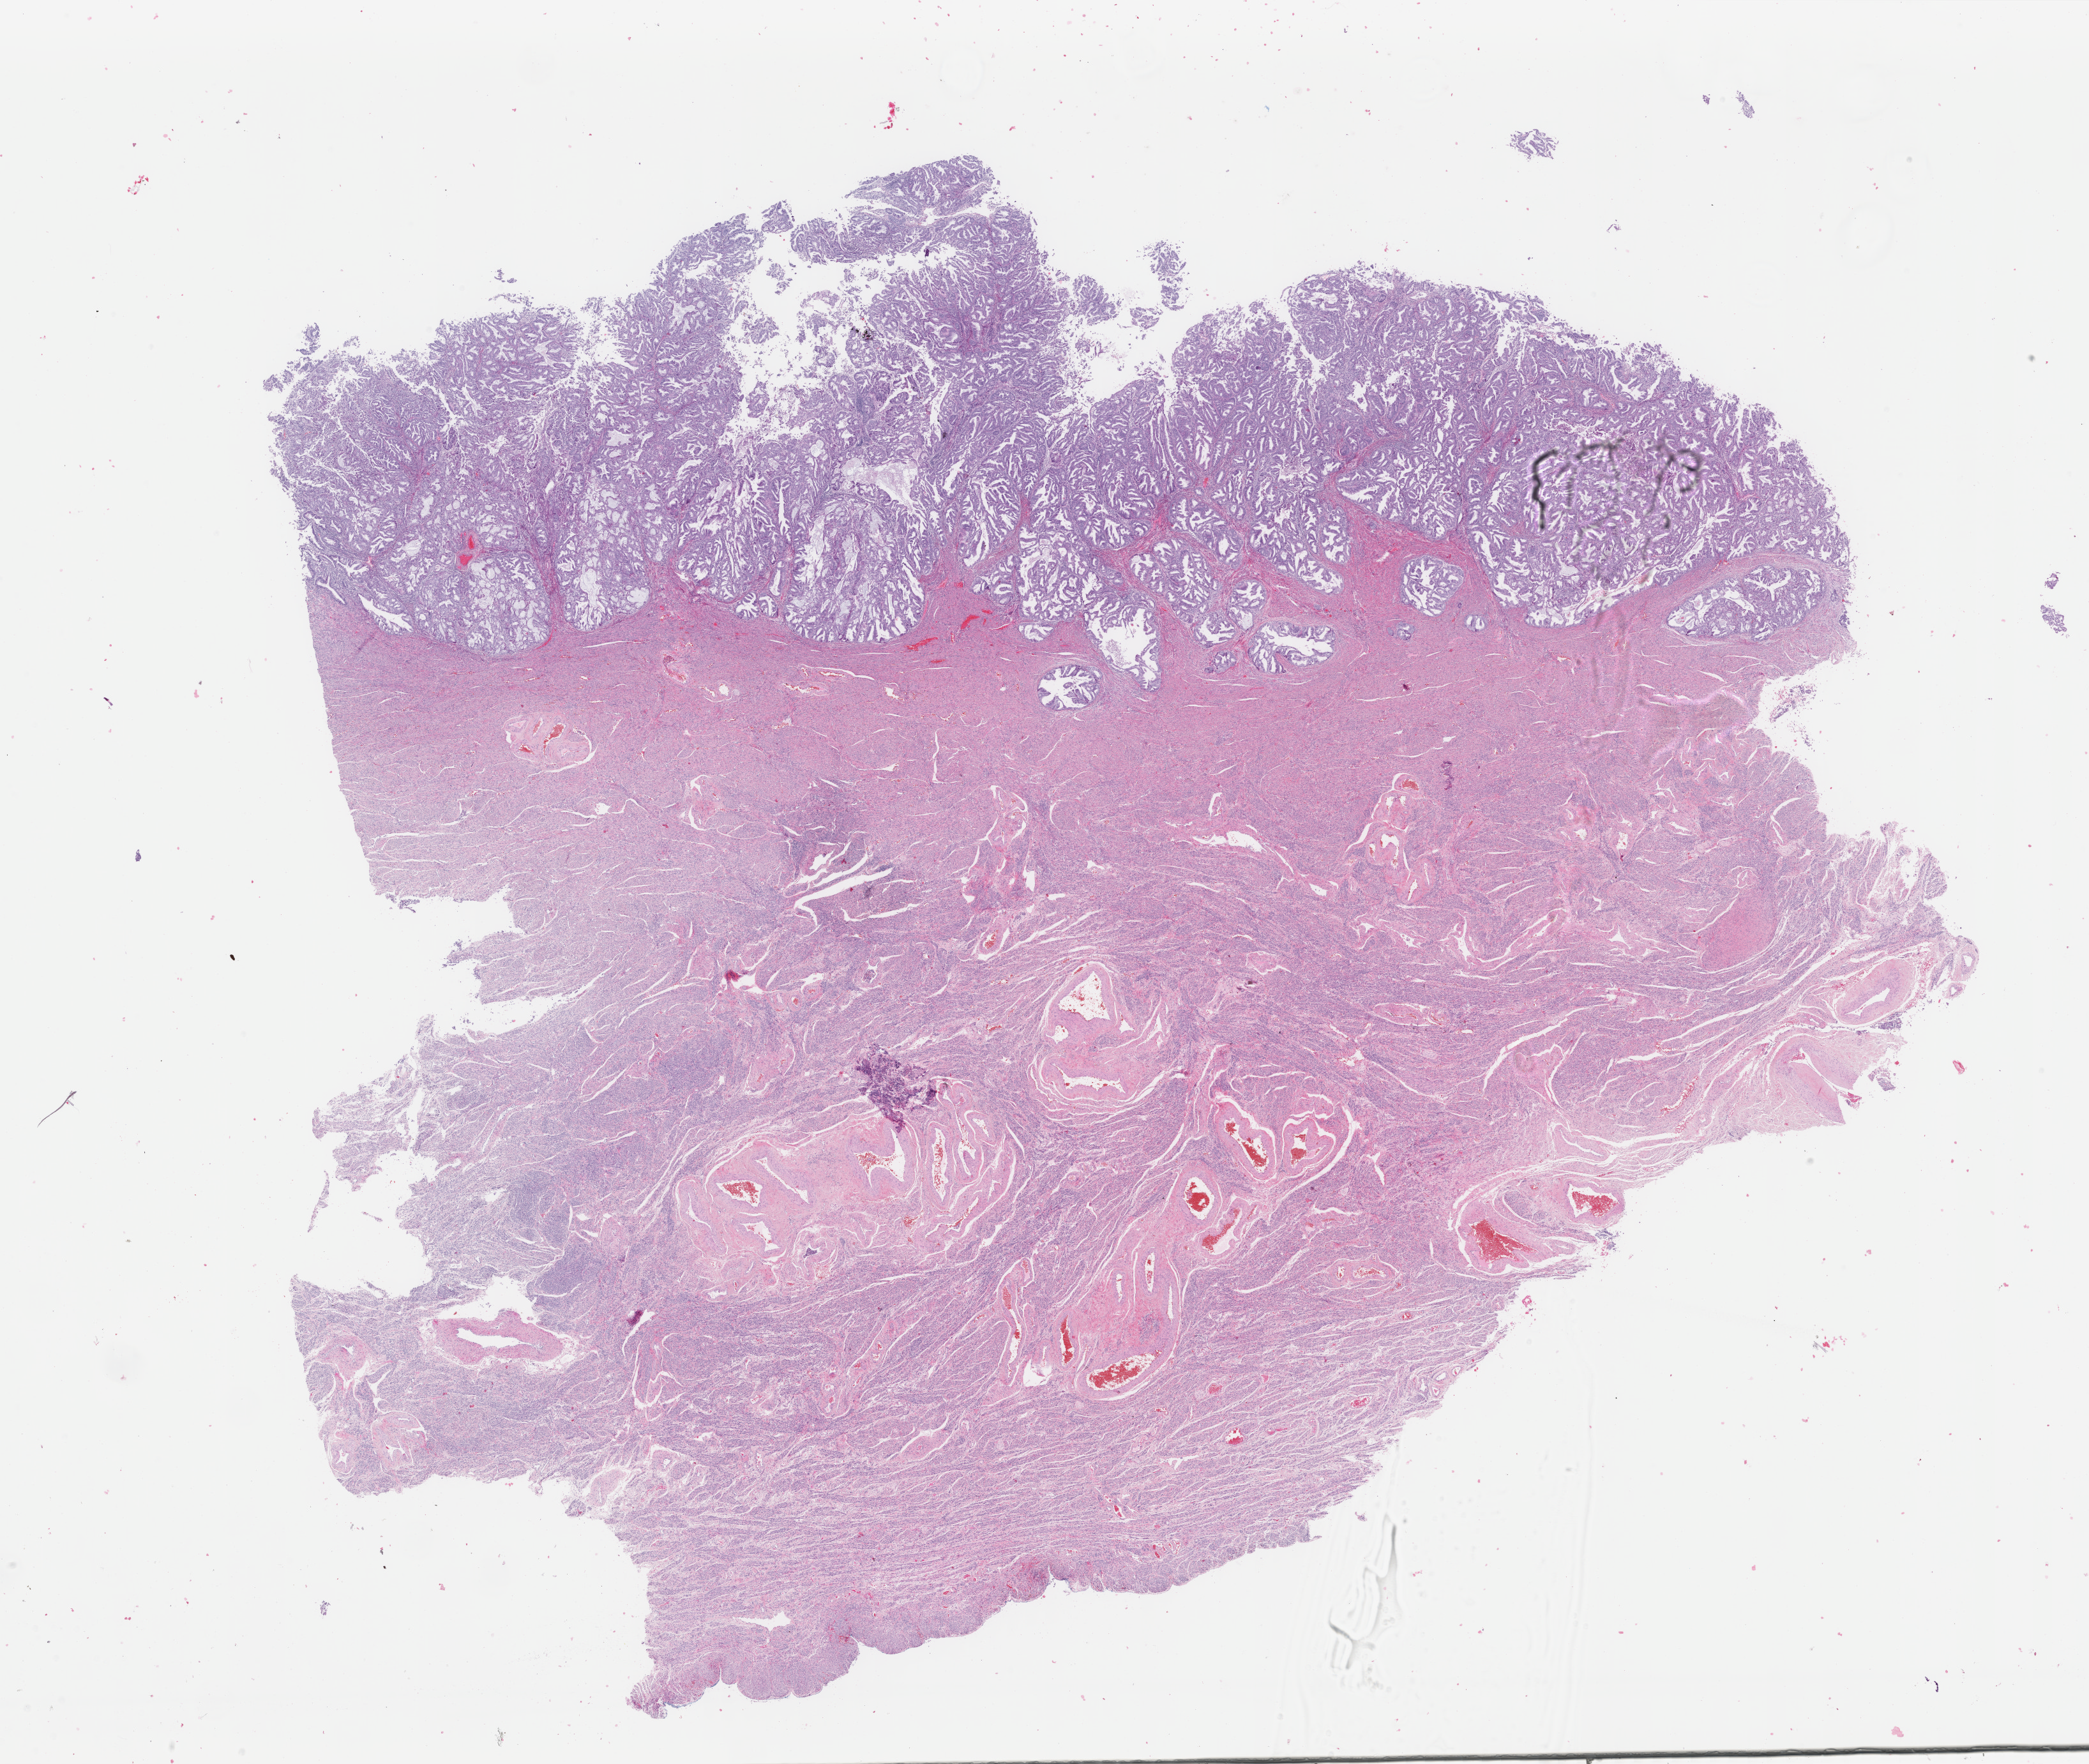
Hematoxylin and eosin (H&E) stained whole-slide image, low-resolution overview of the scanned area, about 26.0 x 21.9 mm (acquisition: 40x scan). Formalin-fixed paraffin-embedded (FFPE) diagnostic section. Primary tumour sample from the uterus. Patient: female, age at initial diagnosis 63 years. Histologic grade: G1 (well differentiated).
- FIGO stage: IIIA
- pathologic diagnosis: Endometrioid adenocarcinoma, NOS (endometrium)